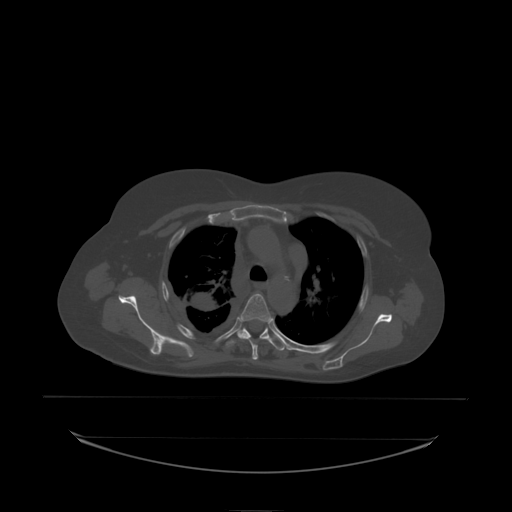
CT including the spine, one axial slice; slice 163 of 242 in the series (ordered by position); bone window (W 1800 / L 400 HU); 2.5 mm slice thickness; 512 × 512 image matrix, field of view 500 × 500 mm. Female patient, age 53 years. Case-level facts recorded for this patient, not image findings: primary cancer: lung; vertebrae with lytic lesions (as recorded): T7, L1.
Outlined on this slice (semi-automatic segmentation, software-assisted and operator-edited):
- T4 vertebra: bounding box (x1, y1, x2, y2) in pixels: (240, 294, 272, 324)
- T5 vertebra: (237, 328, 270, 338)